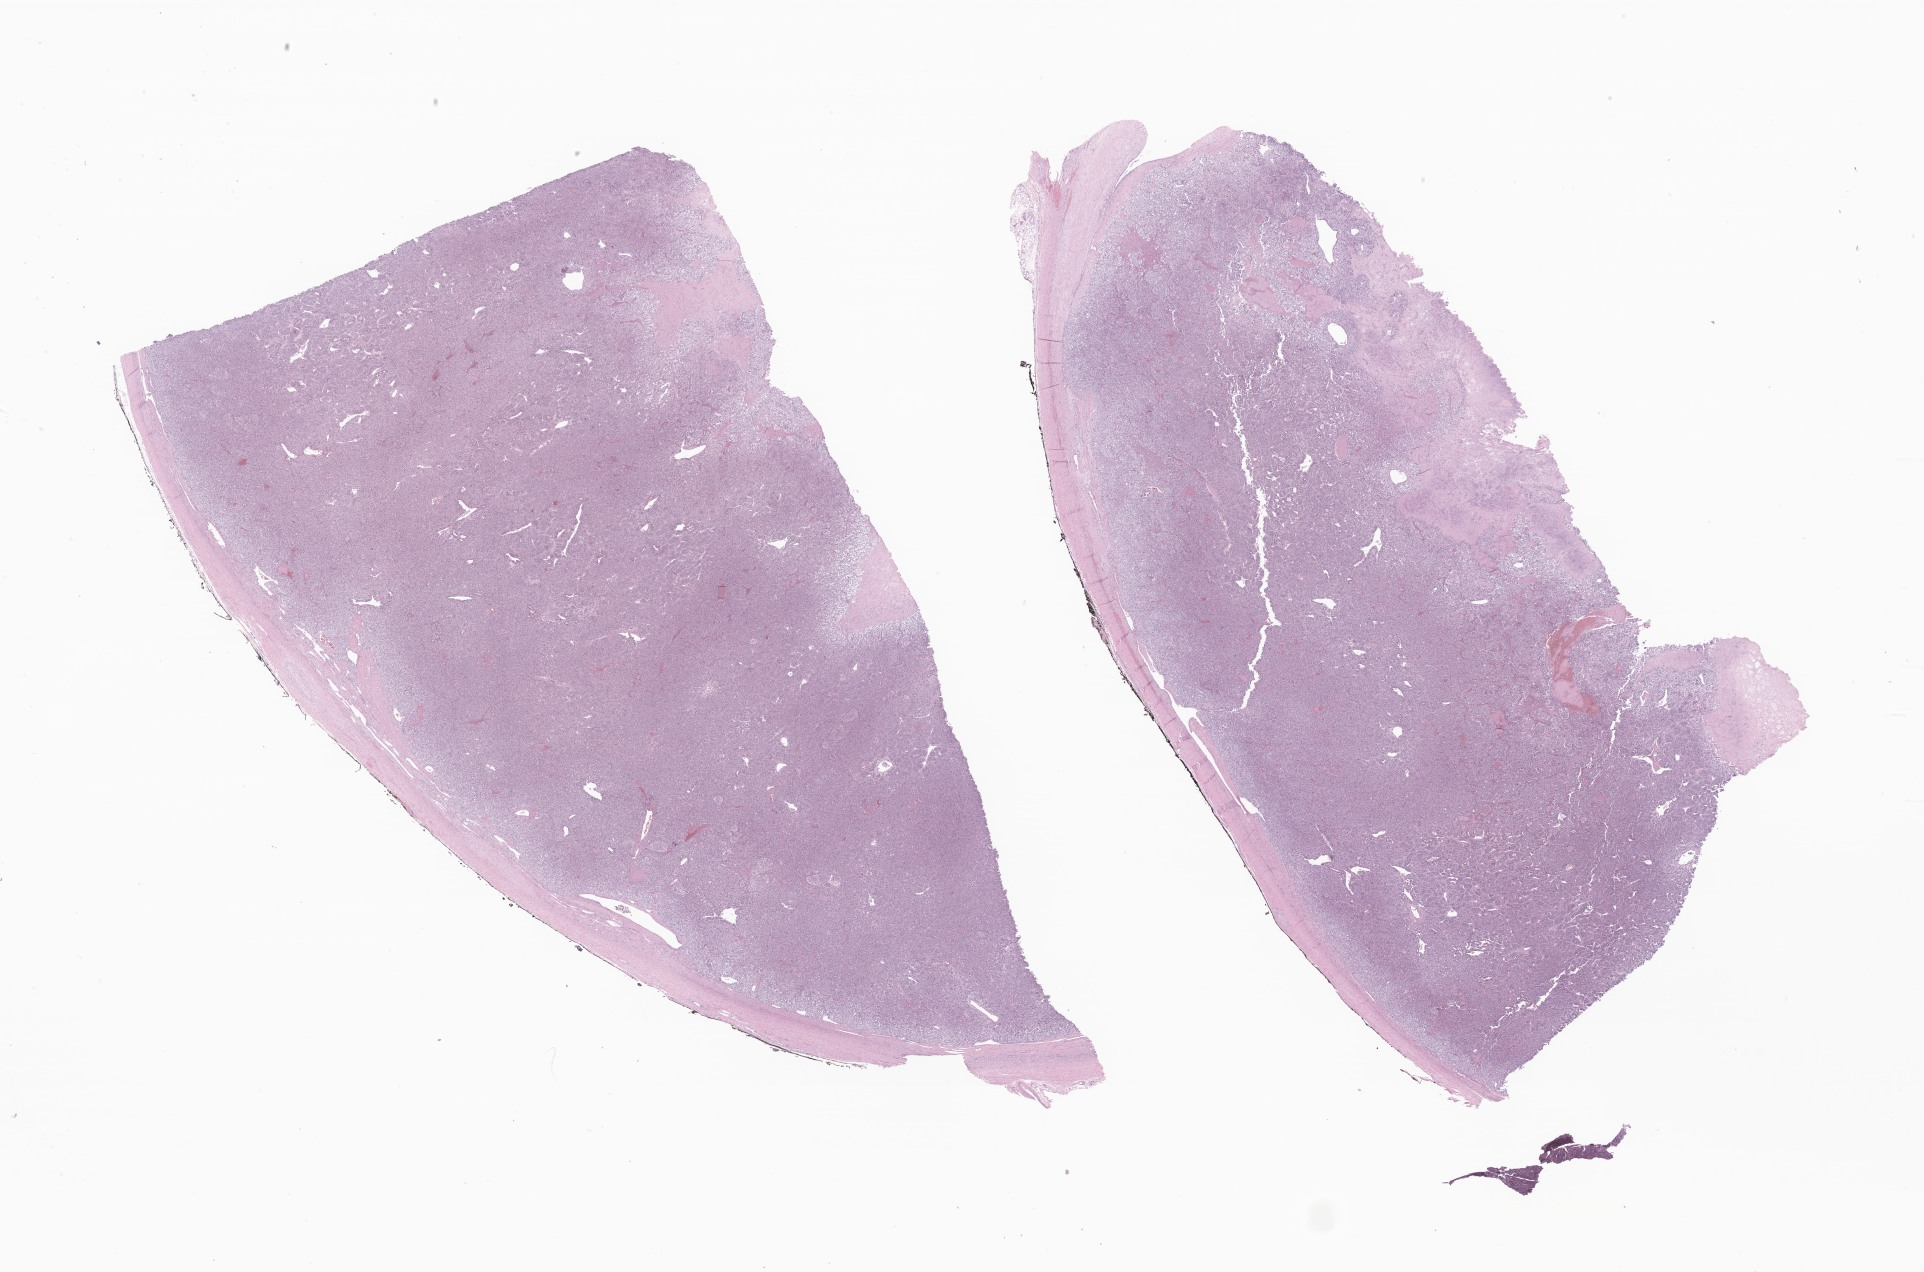
H&E whole-slide image of tumor tissue from the adrenal gland — shown as a low-resolution overview of the whole scanned area (about 32.5 x 21.5 mm); formalin-fixed, paraffin-embedded (FFPE) tissue. Female patient, age 187 months.
Diagnosis: Pheochromocytoma, NOS.